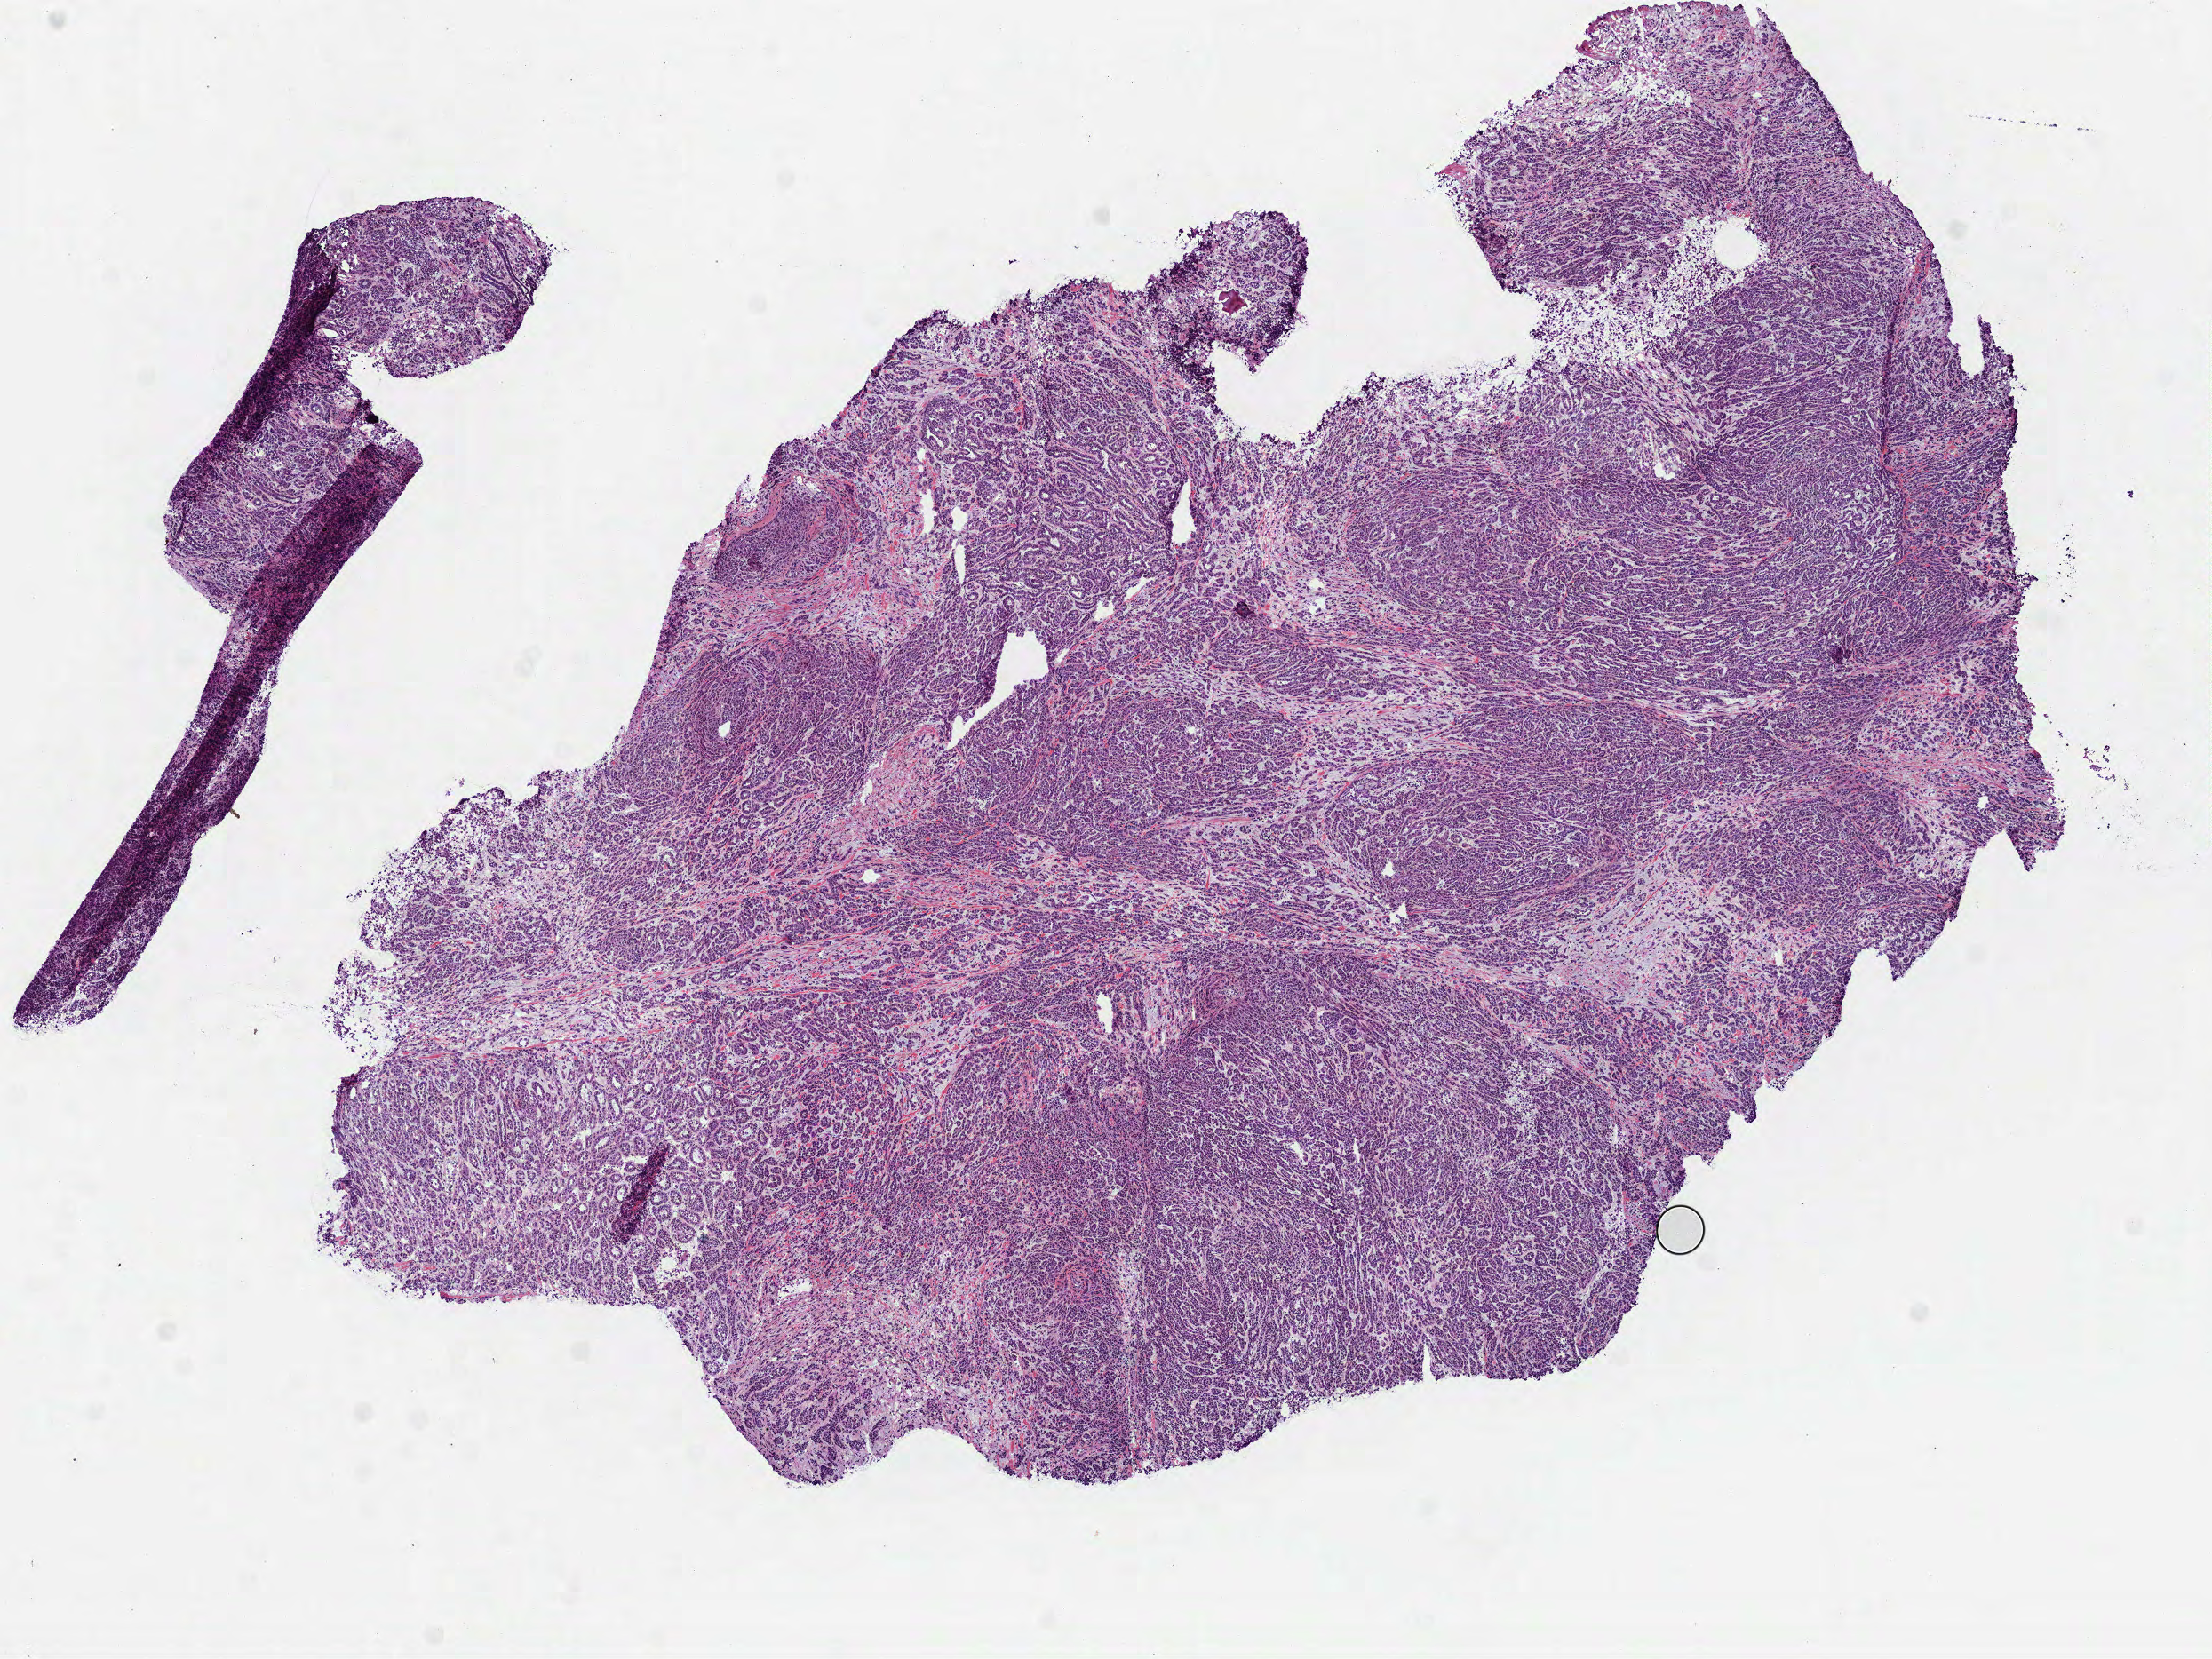
Whole-slide histology image, H&E, whole scanned area (about 10.0 x 7.5 mm, from a 40x scan) shown as a low-resolution overview. Frozen section from the bottom of the tissue portion. Kidney, primary tumour sample. Female patient; age at initial diagnosis 28 years. Composition of this section per pathologist review: tumour cells 100%, tumour nuclei 90%, normal cells 0%, stromal cells 0%, necrosis 0%. Infiltration values recorded for this section: lymphocyte infiltration 2%, monocyte infiltration 0%, neutrophil infiltration 0%.
Histologic diagnosis: Papillary adenocarcinoma, NOS. AJCC pathologic stage: III.